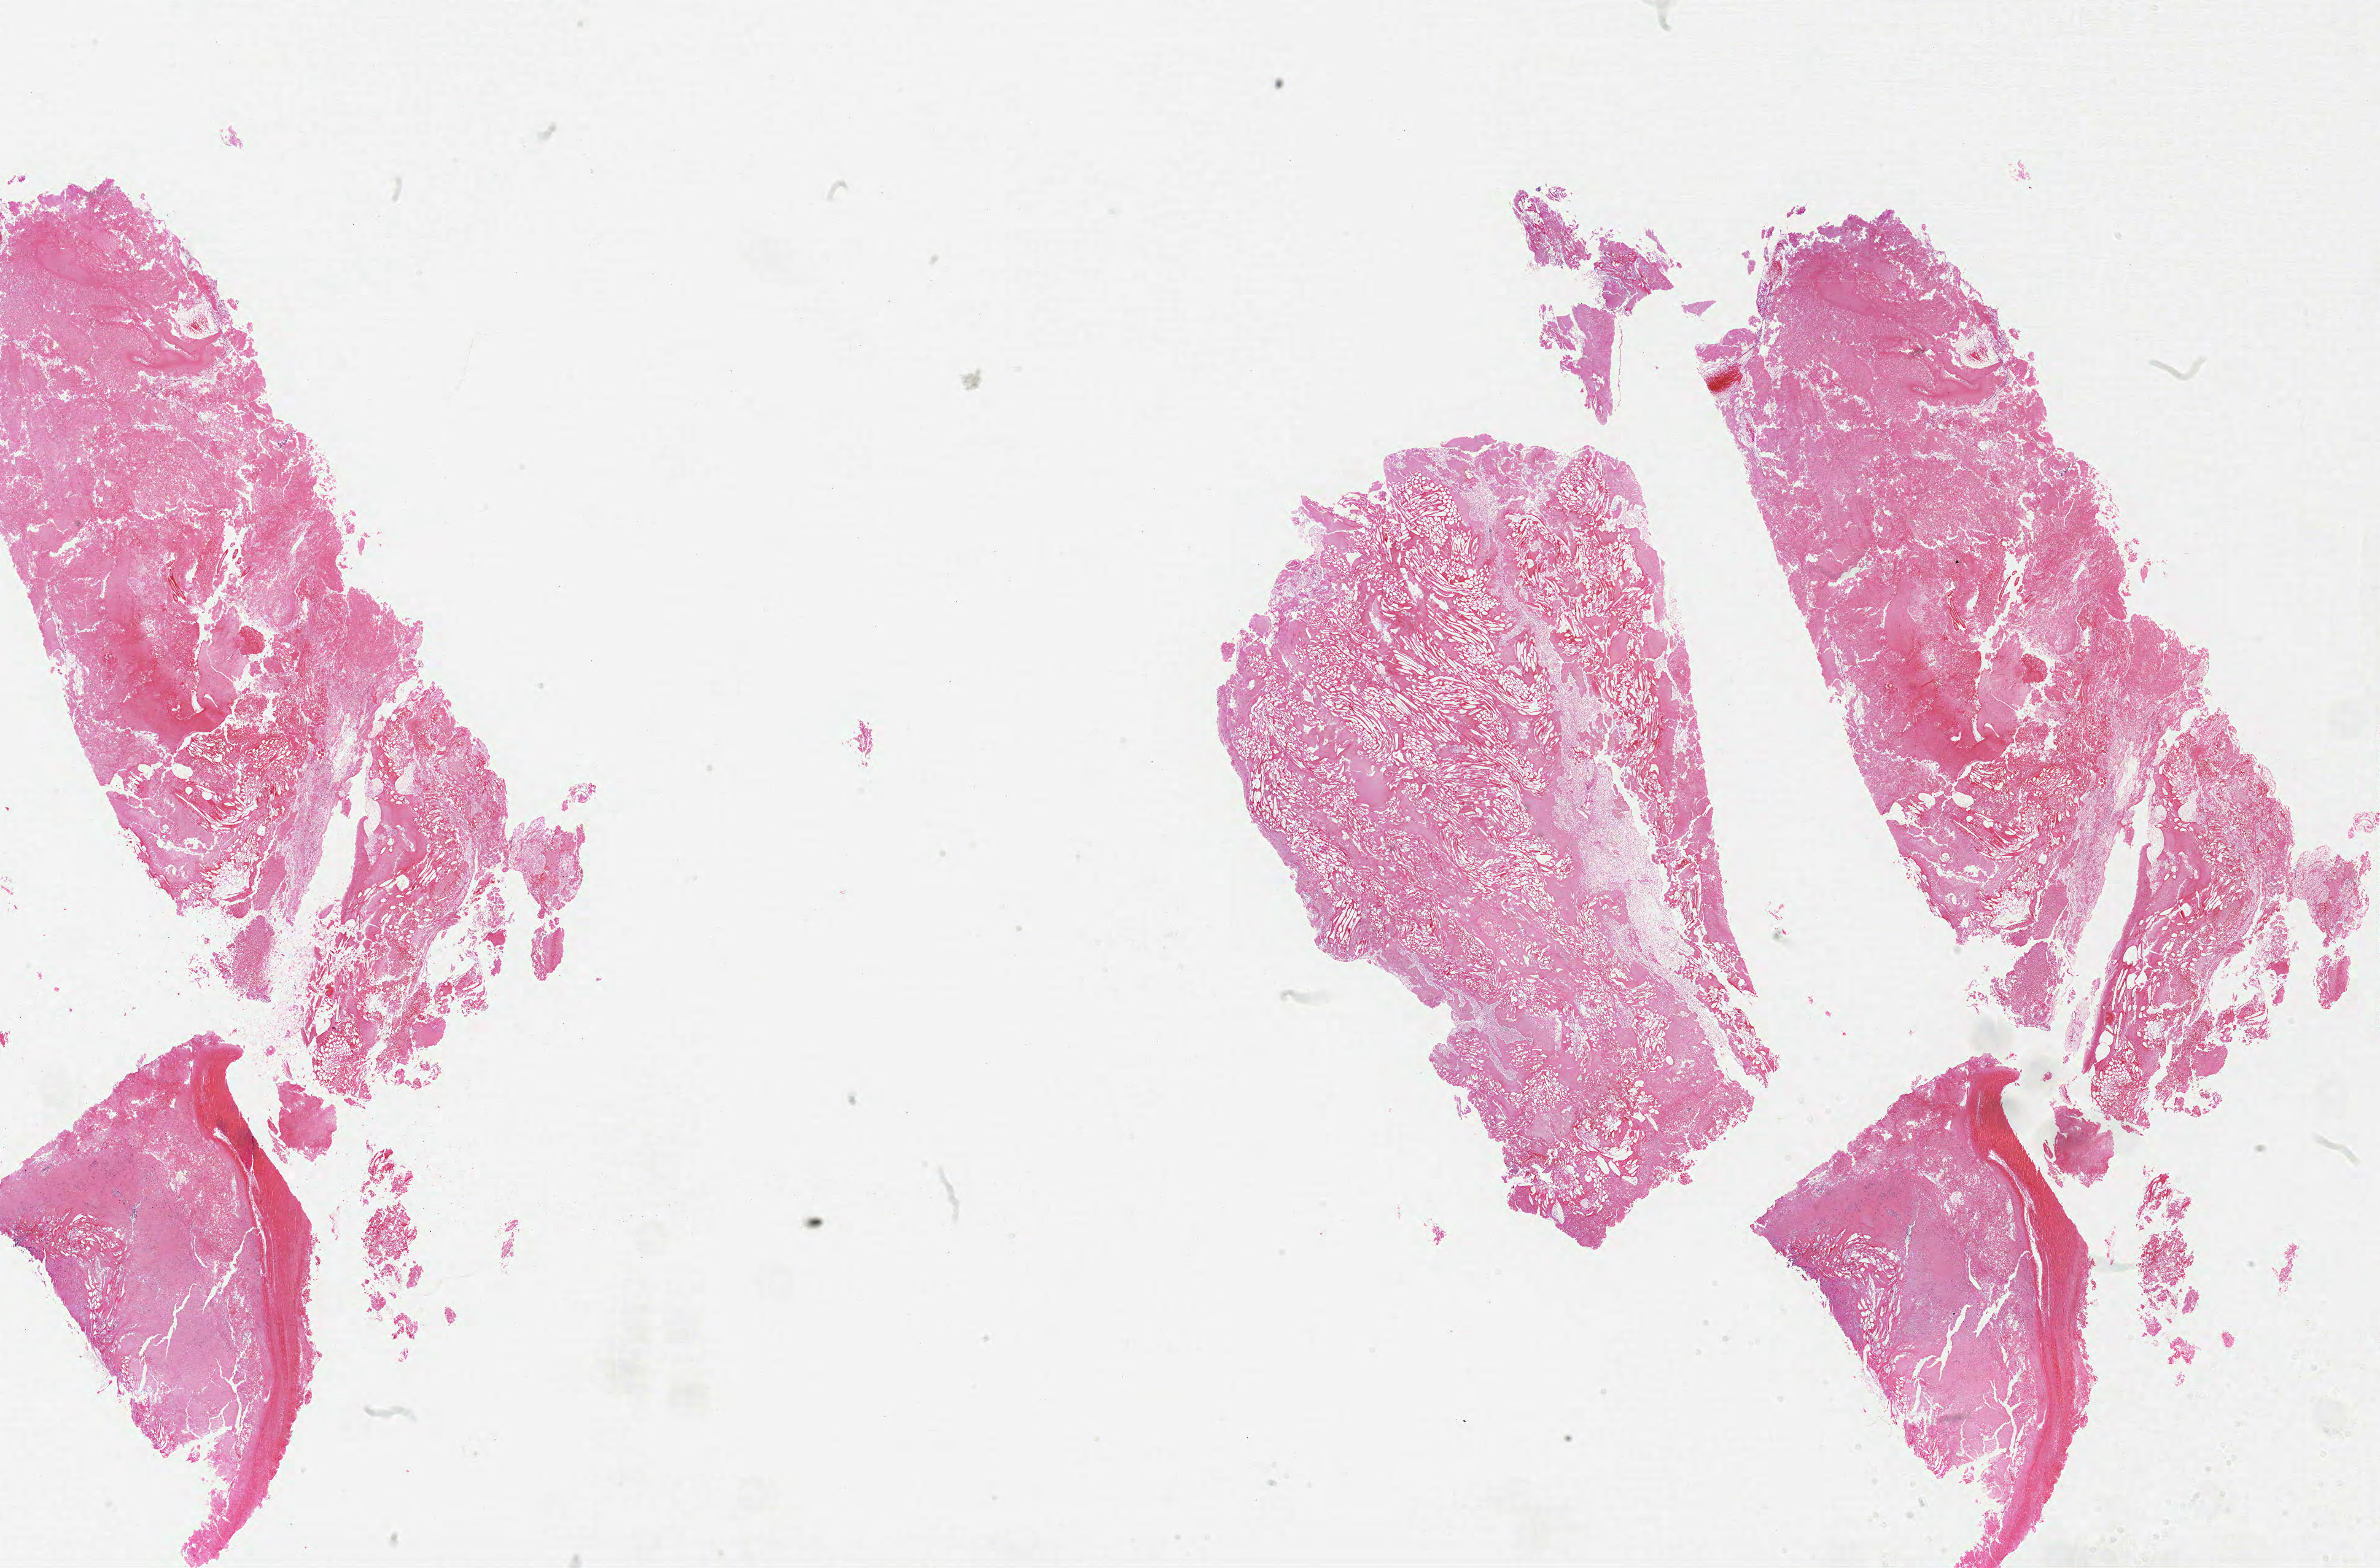
H&E whole-slide image, shown as a low-resolution overview of the whole scanned area (about 31.0 x 20.4 mm), formalin-fixed paraffin-embedded (FFPE) diagnostic section, brain, primary tumour sample. Patient: female, age at initial diagnosis 48 years.
Diagnosis: Glioblastoma.